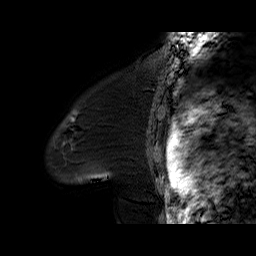
Breast MRI (dynamic contrast-enhanced), one sagittal slice; slice 51 of 60 in the series (ordered by position); dynamic contrast-enhanced series, time point 2 of 6 at this slice position (early post-contrast); 1.5 T; TE 6.2 ms, TR 32.4 ms; 256 × 256 image matrix, field of view 200 × 200 mm. Female patient. Case-level facts recorded for this patient, not image findings: setting: breast cancer imaged before/during neoadjuvant chemotherapy; receptor status: triple-negative.
Annotated regions visible in this slice (semi-automatically segmented with operator editing):
- analysis volume of interest (the breast-tissue region the enhancement analysis was run in; not a lesion): bounding box (x1, y1, x2, y2) in pixels: (47, 97, 134, 184)
- tumour enhancement mask (voxels above the 100 % enhancement threshold inside the analysis volume of interest): (71, 119, 73, 145)